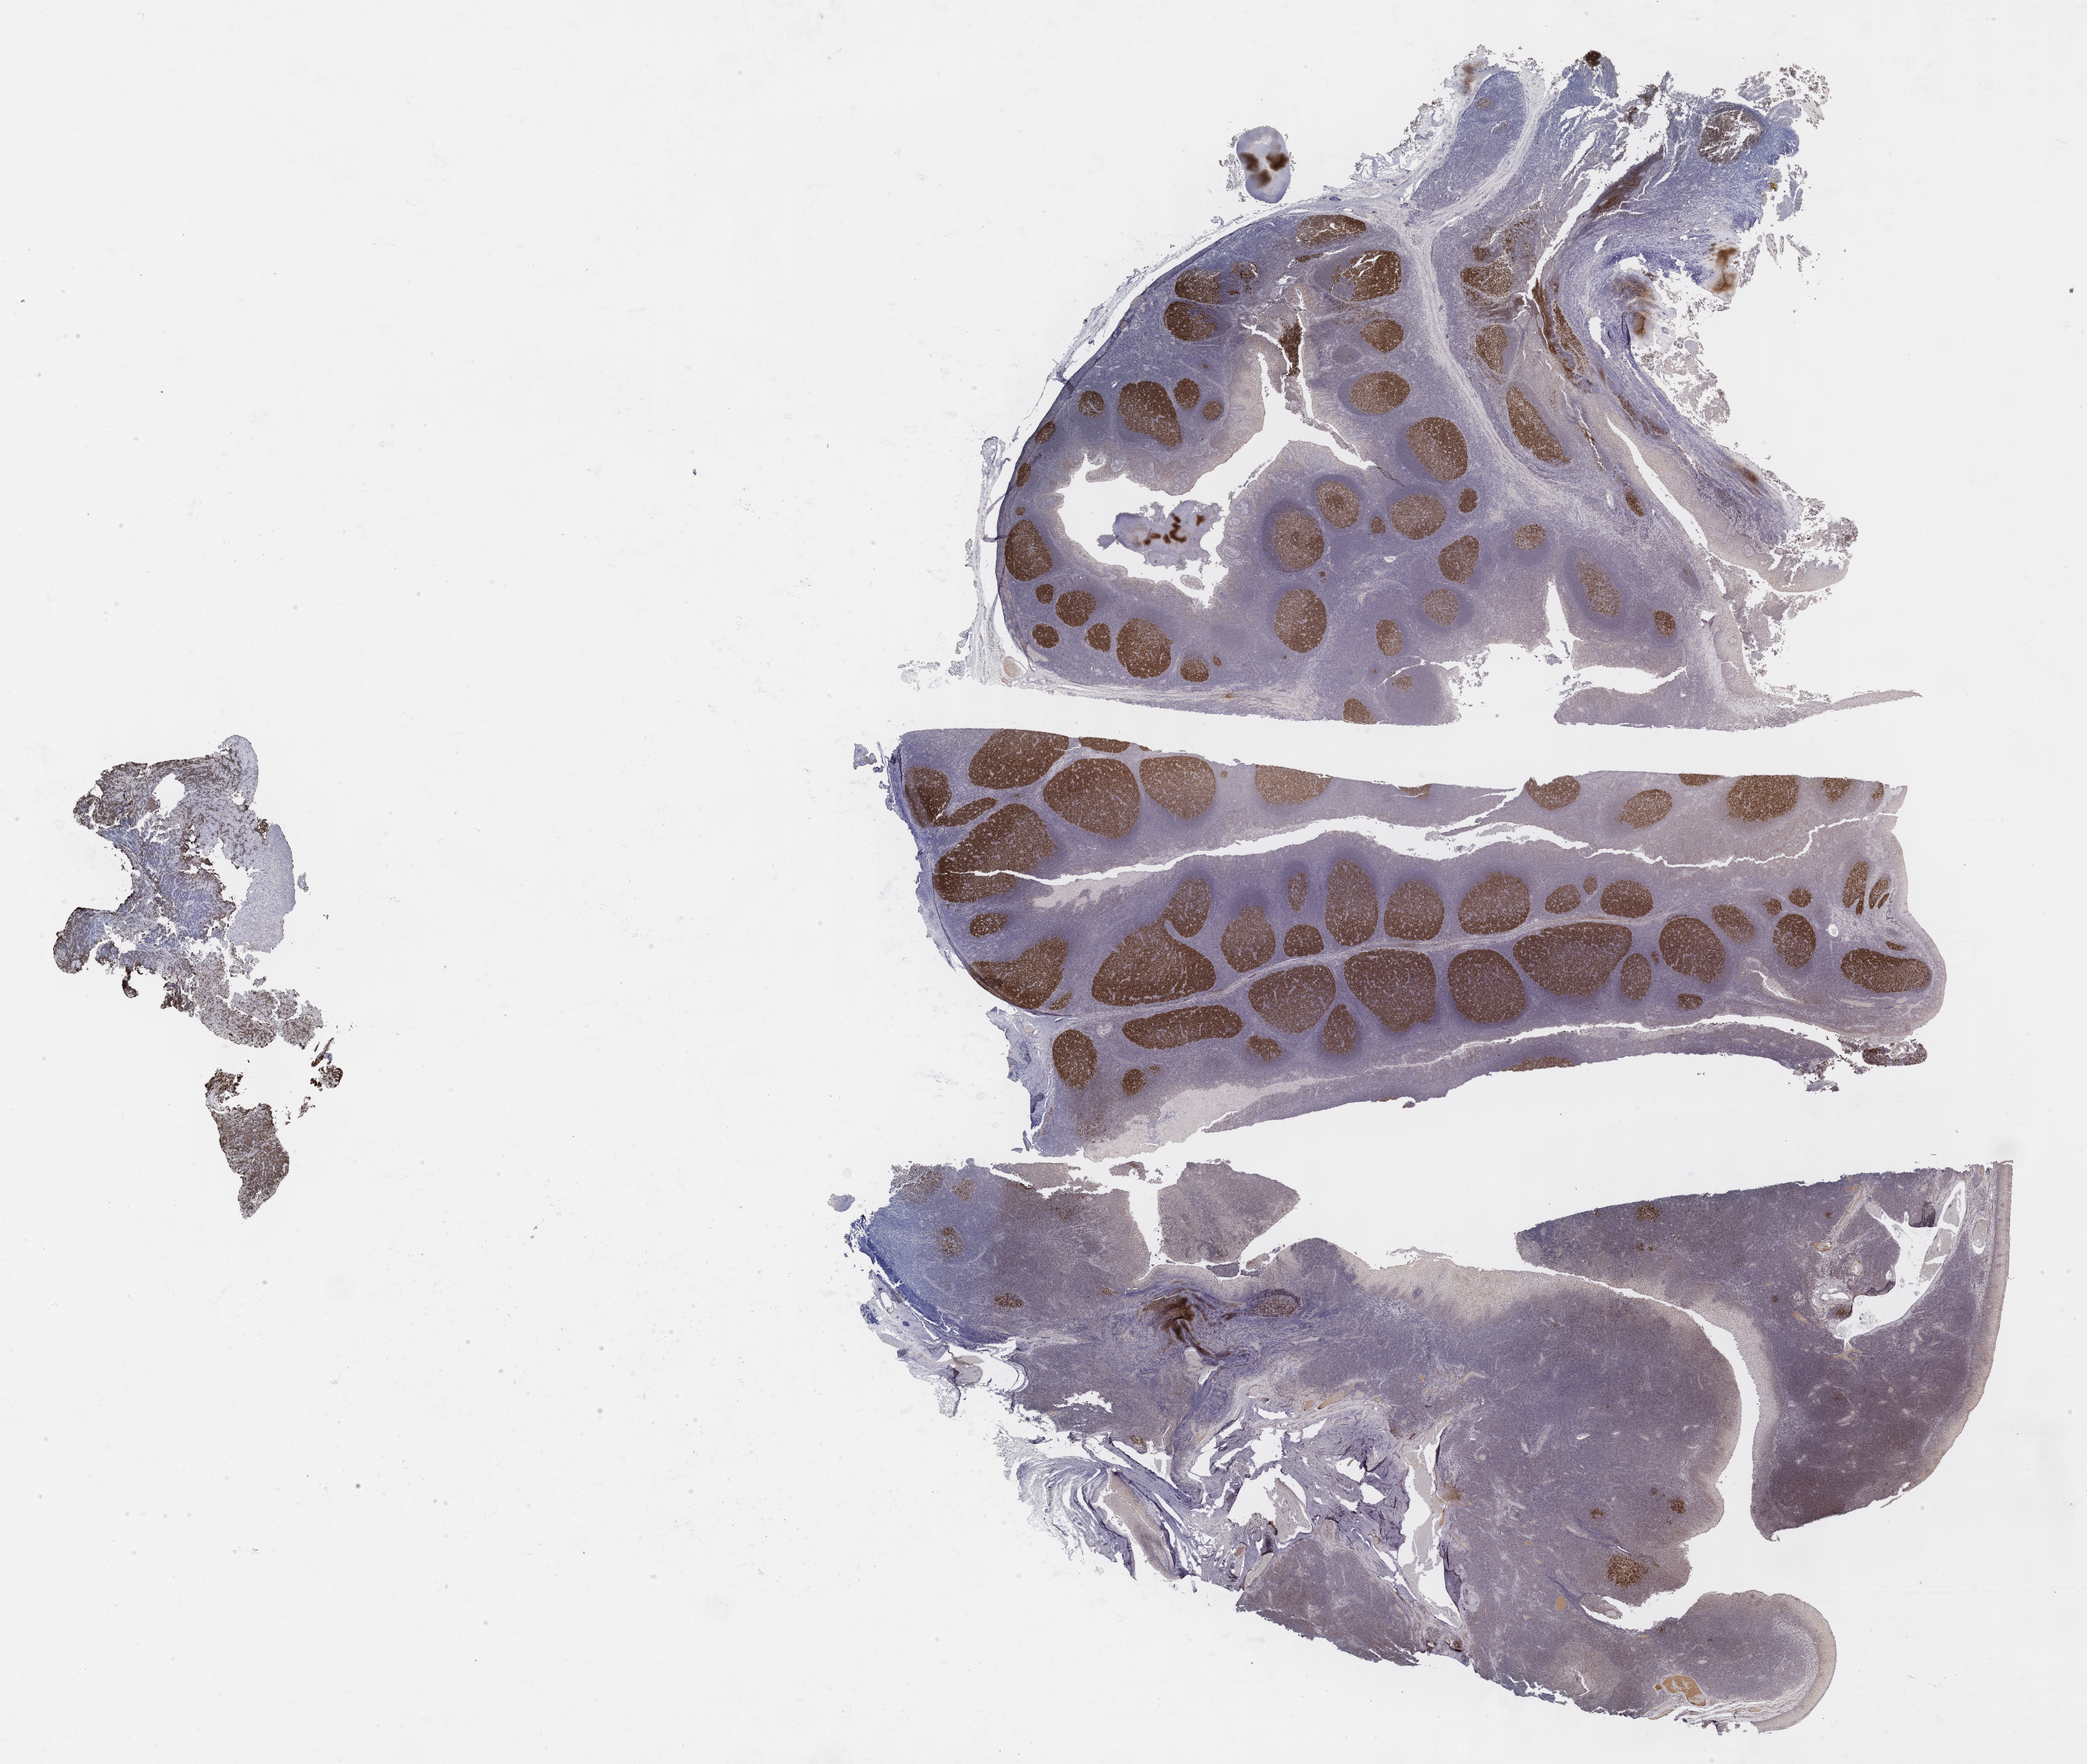
IHC for BCL6, whole-slide image, shown as a low-resolution overview of the whole scanned area (about 25.2 x 21.3 mm). Tumor tissue. Site: gum of mandible. Patient male; 10 years old.
Histologic diagnosis: Burkitt lymphoma, NOS.